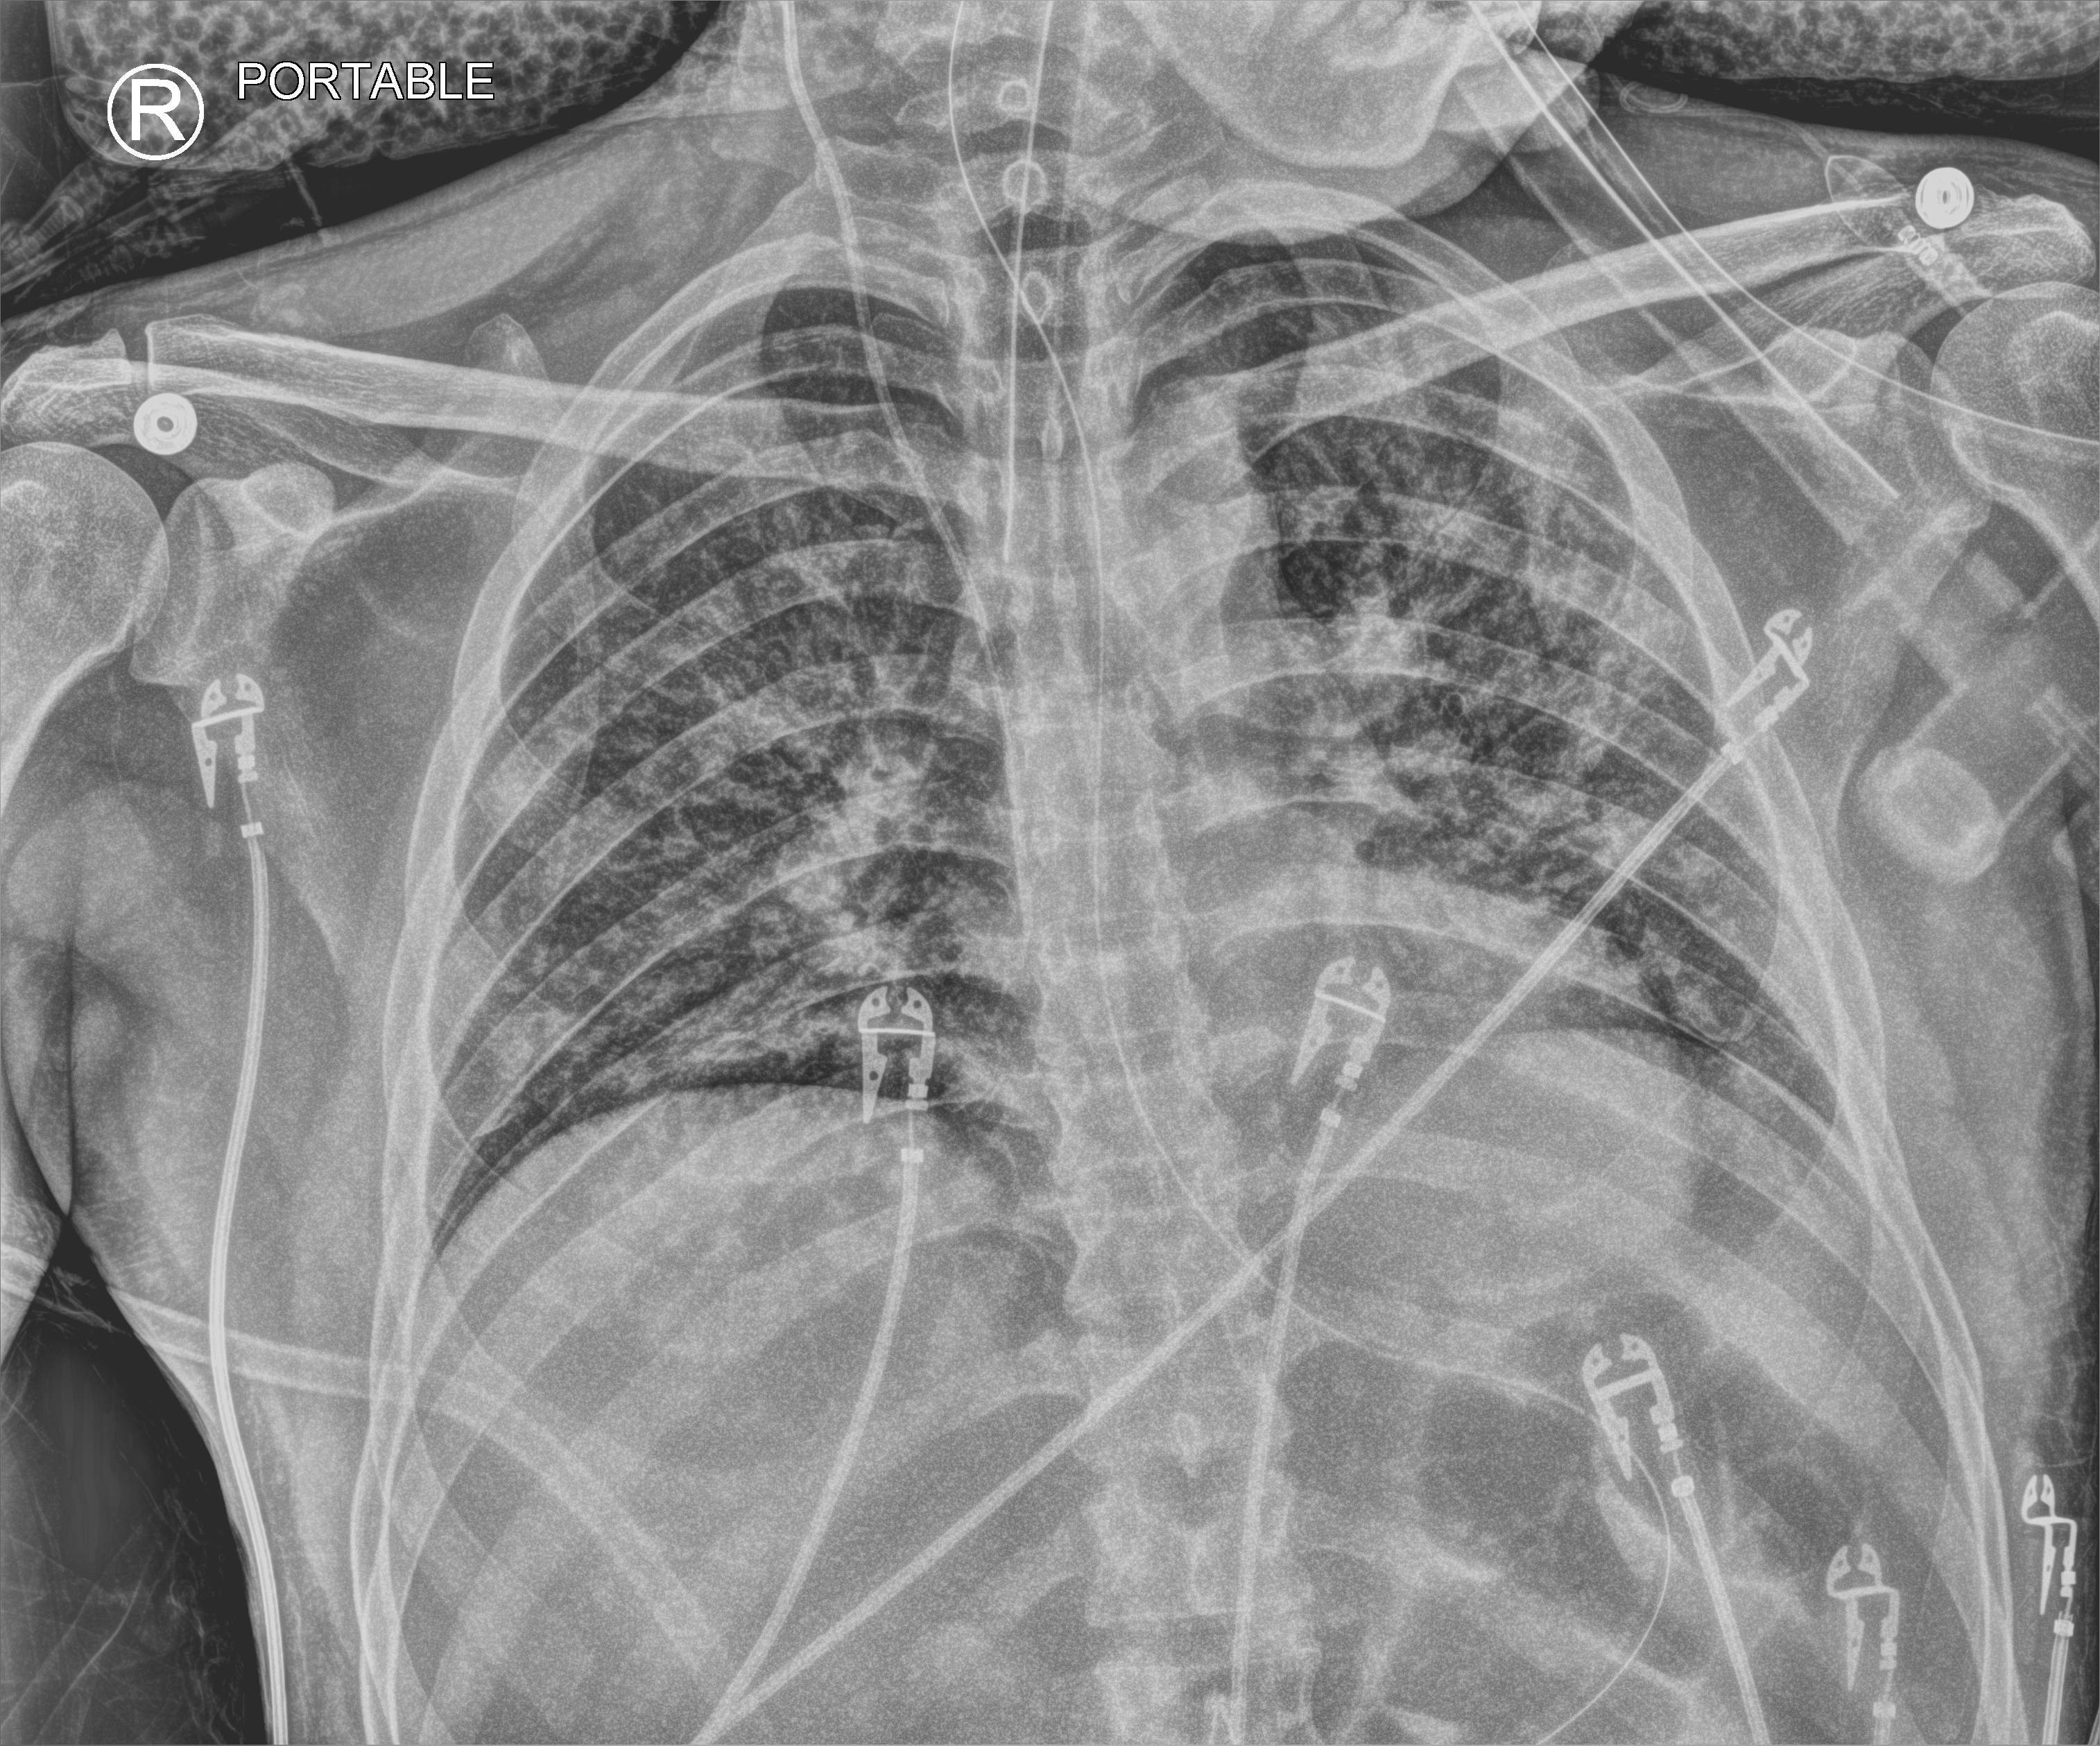
Chest X-ray (portable), anteroposterior (AP) projection. Male patient hospitalised with COVID-19, age 18–59 years.
Hospital-stay facts (about this admission, not read from this image; timing relative to this image not recorded): mechanically ventilated during this hospital stay: yes.